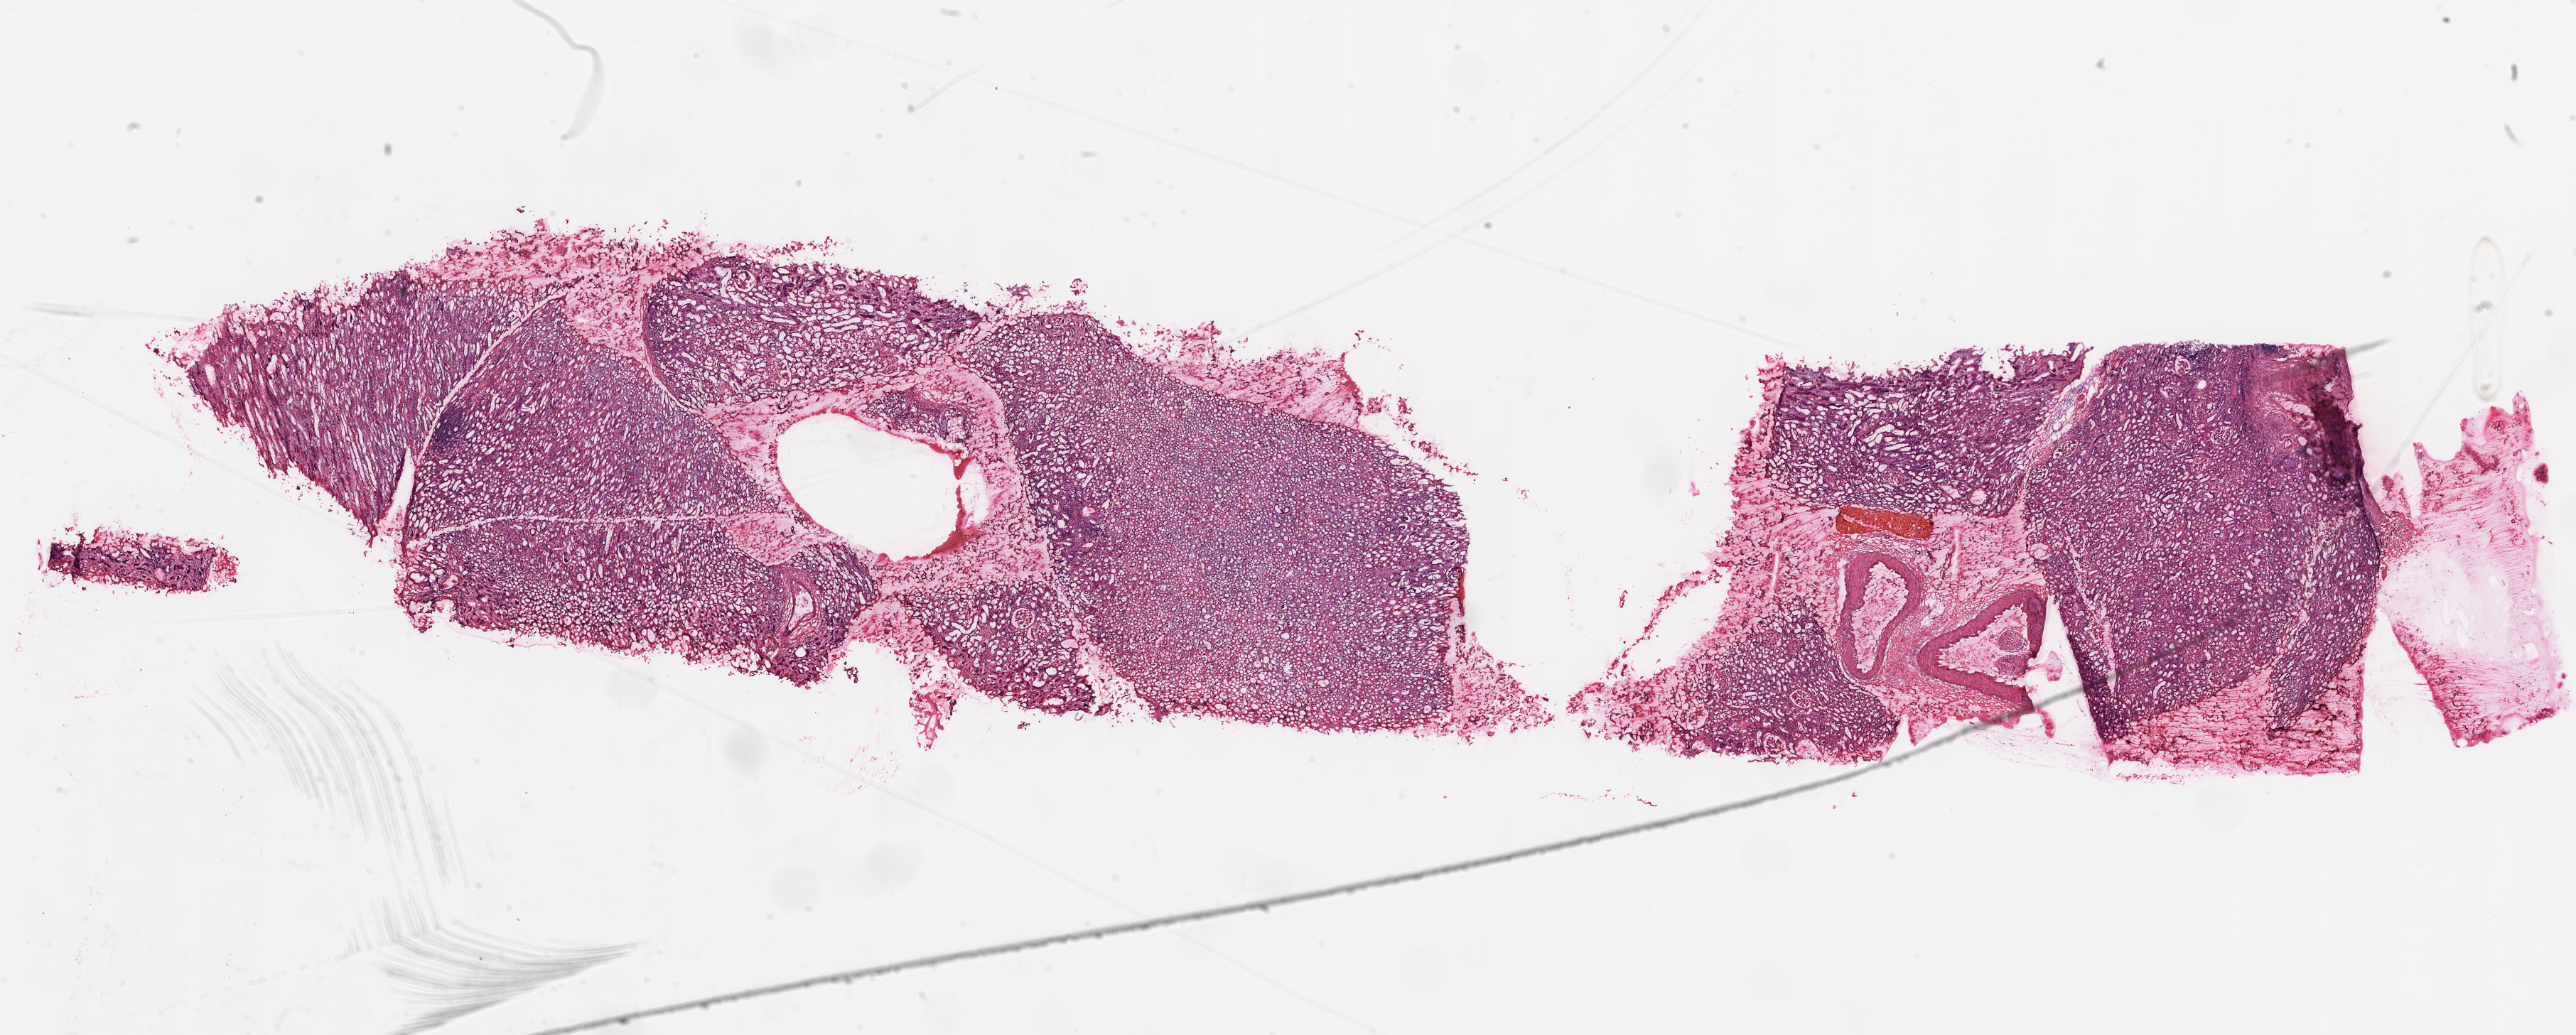
Hematoxylin and eosin (H&E) stained whole-slide image — shown as a low-resolution overview of the whole scanned area (about 29.1 x 11.7 mm); frozen section; sample: solid tissue normal (non-tumour tissue), kidney. Male patient; age at initial diagnosis 41 years.
This section: solid tissue normal sample (biorepository sample class). Patient diagnosis: Clear cell adenocarcinoma, NOS.